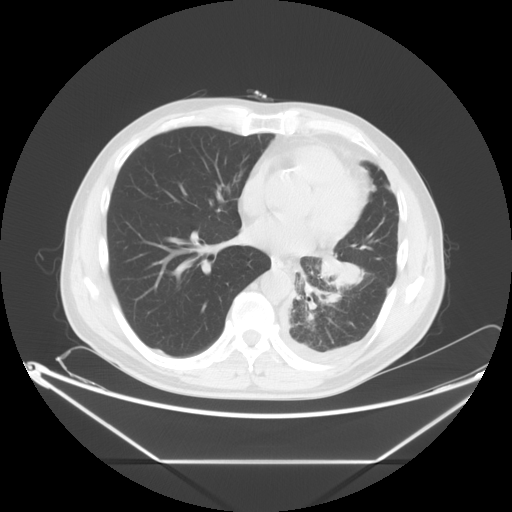
Chest CT, one axial slice. 120 kVp. Lung window (W 1500 / L -600 HU). 5 mm slice thickness. 512 × 512 image matrix, field of view 442 × 442 mm. Male patient, age 60 years. Case-level facts recorded for this patient, not image findings: clinical TNM (as recorded): T4 N1 M1.
Outlined on this slice (bounding box drawn by a radiologist):
- lung tumour (recorded histology: adenocarcinoma): bounding box [x1, y1, x2, y2] px = [305, 246, 375, 301]